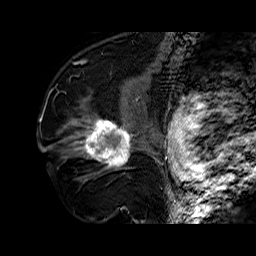
Breast MRI (dynamic contrast-enhanced), one sagittal slice. Position 38 of 60 along the scan axis. Dynamic contrast-enhanced series, time point 2 of 6 at this slice position (early post-contrast). 1.5 T. TE 6.4 ms, TR 32.7 ms. 4 mm slice thickness. 256 × 256 image matrix, field of view 200 × 200 mm. Female patient. Case-level facts recorded for this patient, not image findings: setting: breast cancer imaged before/during neoadjuvant chemotherapy; receptor status: HR-positive, HER2-negative.
Outlined on this slice (semi-automatically segmented with operator editing):
- analysis volume of interest (the breast-tissue region the enhancement analysis was run in; not a lesion): bounding box <73,110,141,179> (left, top, right, bottom; pixels)
- tumour enhancement mask (voxels above the 100 % enhancement threshold inside the analysis volume of interest): <76,120,132,167>